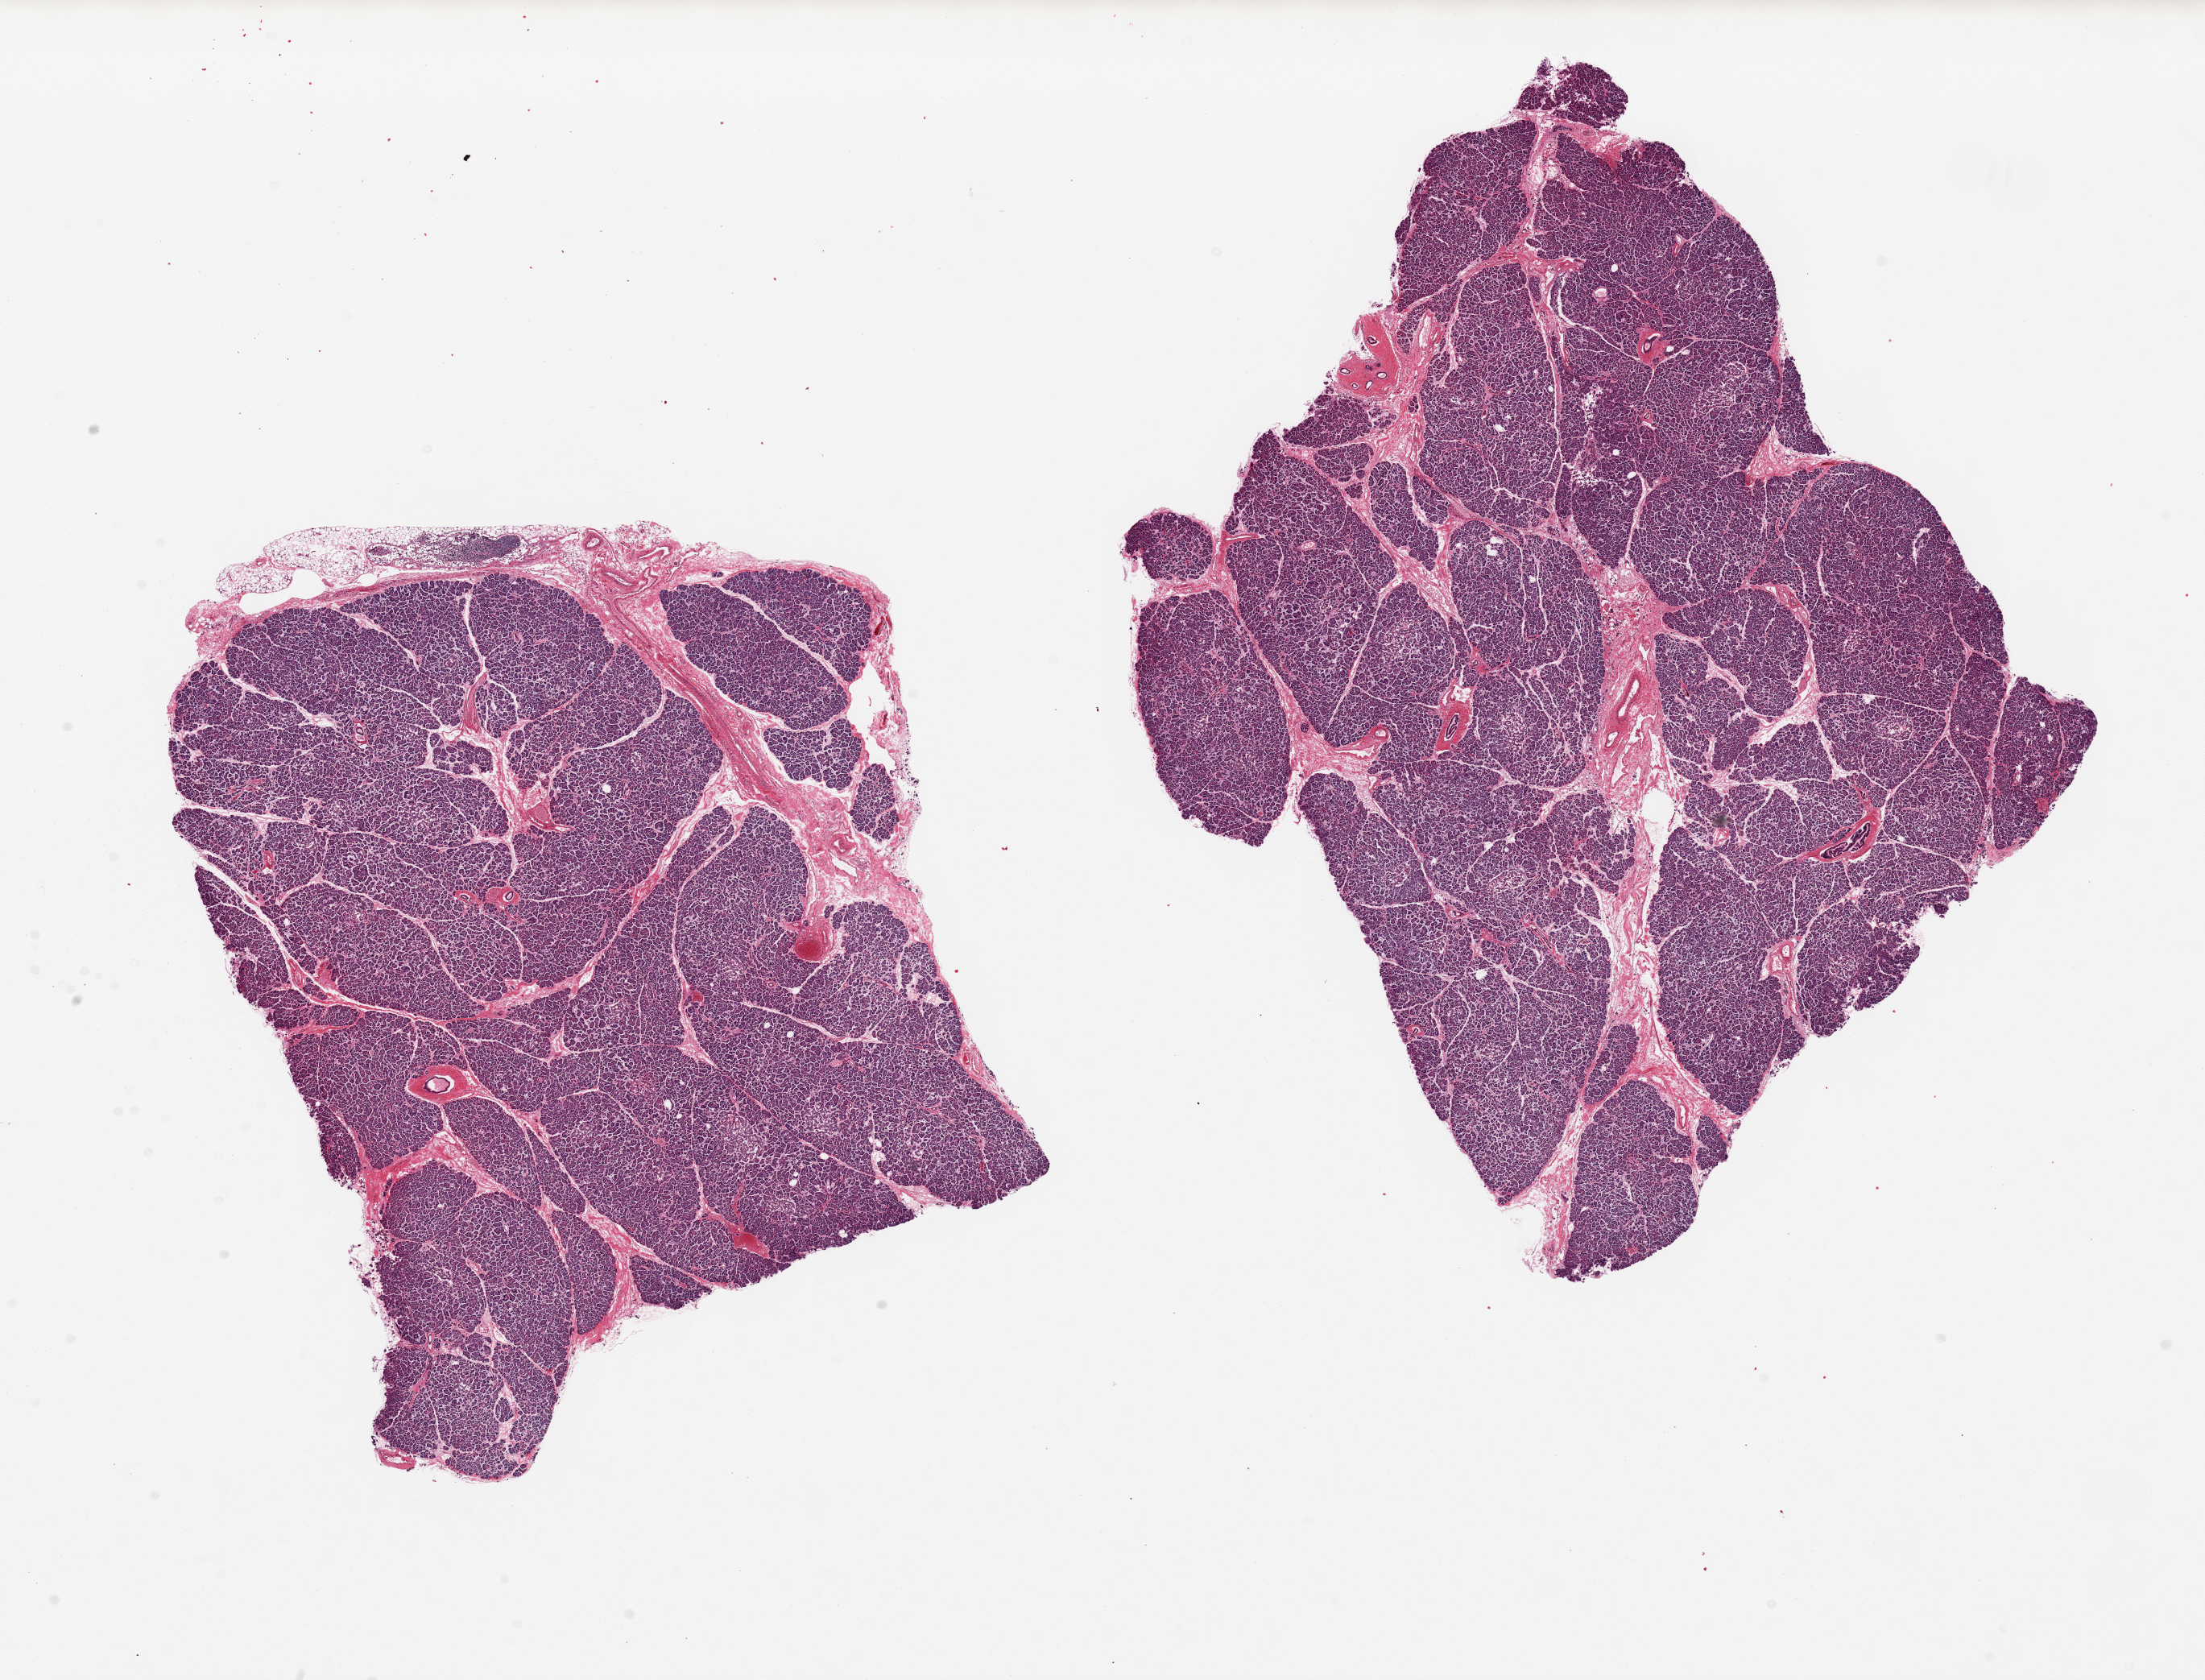
Whole-slide image, H&E stain, brightfield, a low-resolution overview of the entire scanned area, about 21.7 x 16.5 mm; PAXgene-fixed paraffin-embedded (PFPE) section; sampled site (target tissue): pancreas; tissue donor sample. Male donor.
Pathologist's review note for this sample: 2 pieces 9x7 & 8x6 mm.